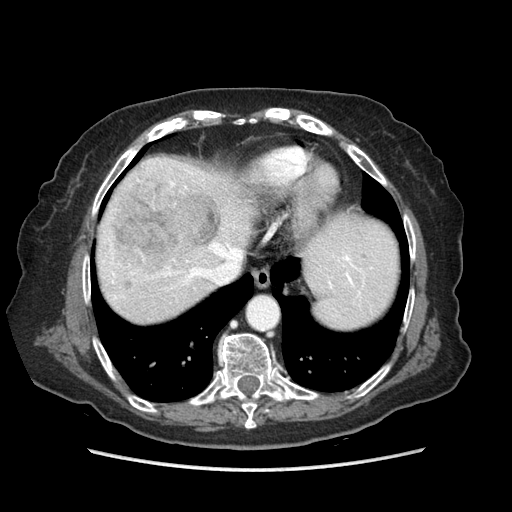
Contrast-enhanced abdominal CT (liver protocol), one axial slice. Position 71 of 89 along the scan axis. Reconstruction kernel STANDARD. Soft-tissue window (W 400 / L 40 HU). 2.5 mm slice thickness. 512 × 512 image matrix. From the clinical record (not read from this slice): diagnosis: hepatocellular carcinoma (patient treated with transarterial chemoembolisation; whether this scan precedes or follows treatment is not stated here); TNM stage (as recorded): Stage-IIIA; Child-Pugh class: A; tumour nodularity: multinodular; tumour size: 11 cm.
Annotated regions visible in this slice (semi-automatically segmented with operator editing):
- abdominal aorta: bounding box (x1, y1, x2, y2) in pixels: (249, 298, 277, 329)
- liver parenchyma outside the tumour (the mass and vessels are separate outlines, so this box may not span the whole liver): (96, 156, 398, 328)
- mass: (110, 171, 221, 291)
- liver vessels: (112, 182, 358, 298)